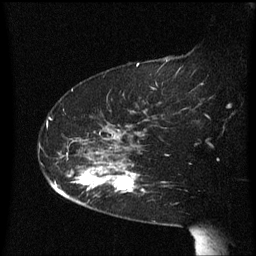
Breast MRI (dynamic contrast-enhanced), one sagittal slice; position 44 of 60 along the scan axis; dynamic contrast-enhanced series, image 2 of 3 at this slice position (ordered by acquisition); 1.5 T; TE 4.2 ms, TR 8.4 ms; 2.3 mm slice thickness; 256 × 256 image matrix. Female patient, age 63 years. Case-level facts recorded for this patient, not image findings: setting: breast cancer imaged before/during neoadjuvant chemotherapy; receptor status: HER2-positive.
Outlined on this slice (semi-automatically segmented with operator editing):
- analysis volume of interest (the breast-tissue region the enhancement analysis was run in; not a lesion): bounding box <71,144,146,207> (left, top, right, bottom; pixels)
- tumour enhancement mask (voxels above the 70 % enhancement threshold inside the analysis volume of interest): <78,164,139,193>